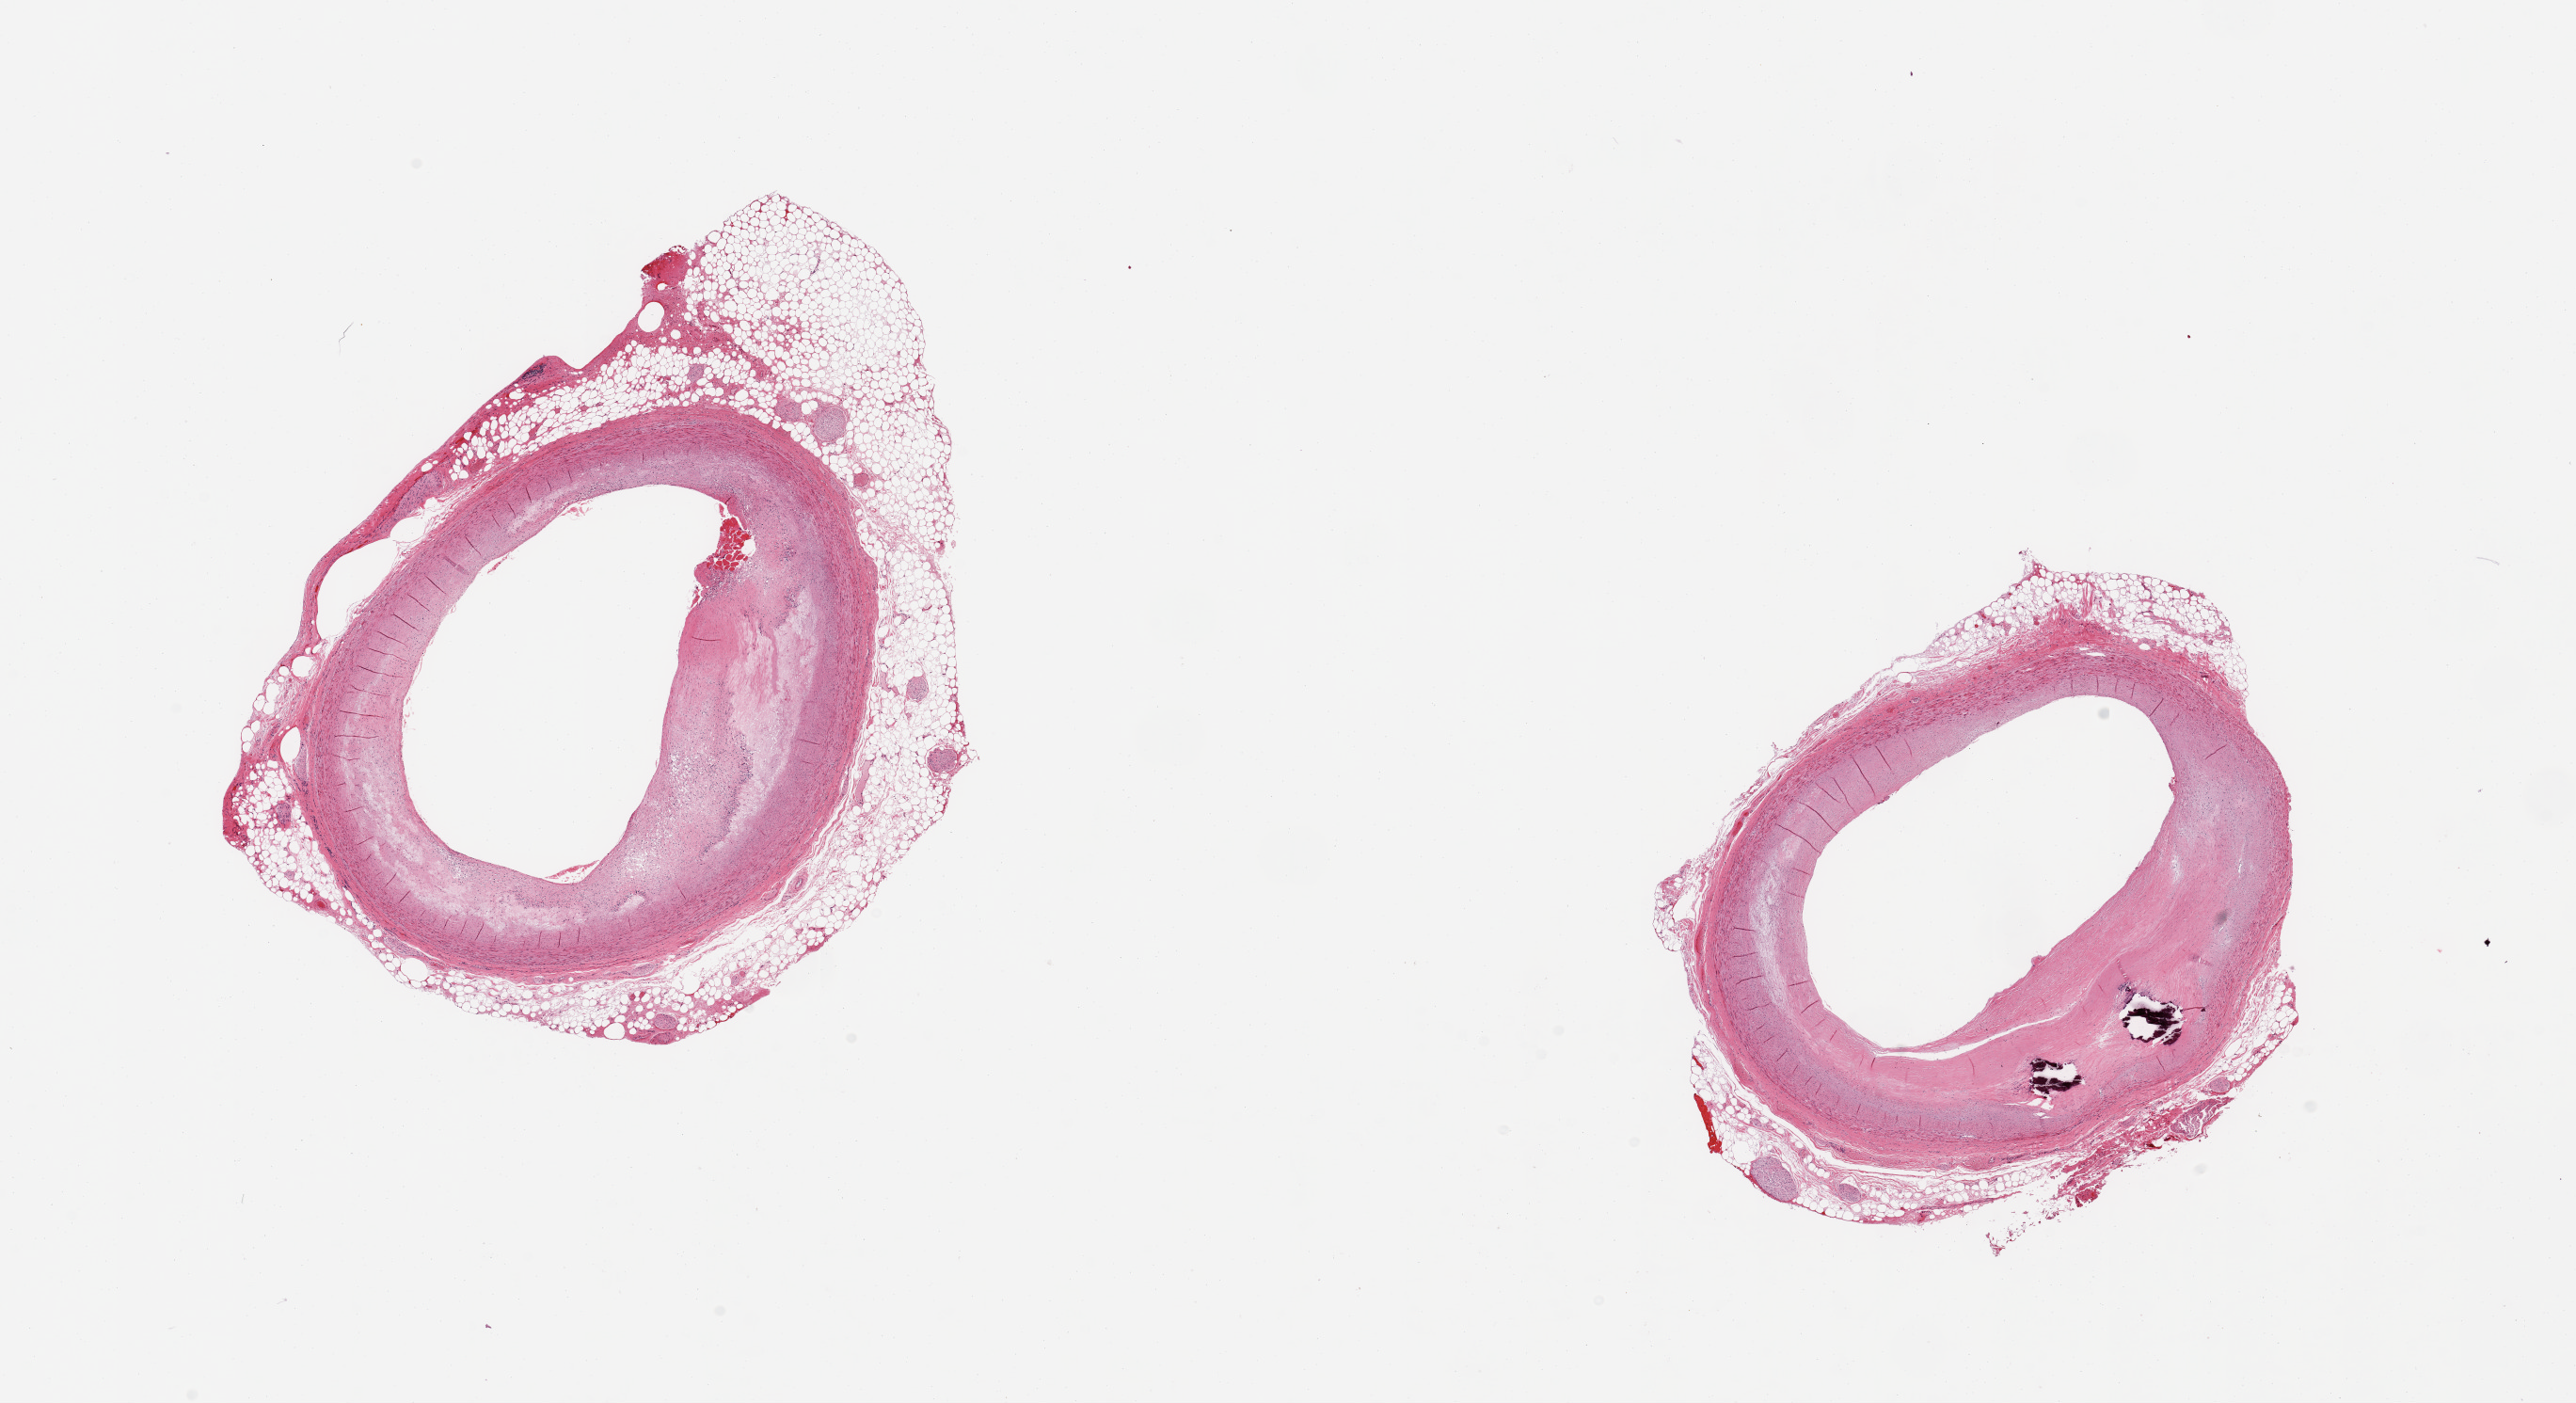
H&E whole-slide image — low-resolution overview of the scanned area, about 21.7 x 11.8 mm (slide scanned at 20x), PAXgene-fixed paraffin-embedded (PFPE) section, sampled site (target tissue): coronary artery, donor tissue sample. Donor: male.
* reviewer comment on this tissue sample: 2 pieces; eccentric plaques with calcific foci occupy 50% area; untrimmed external fat up to 1.6mm thick